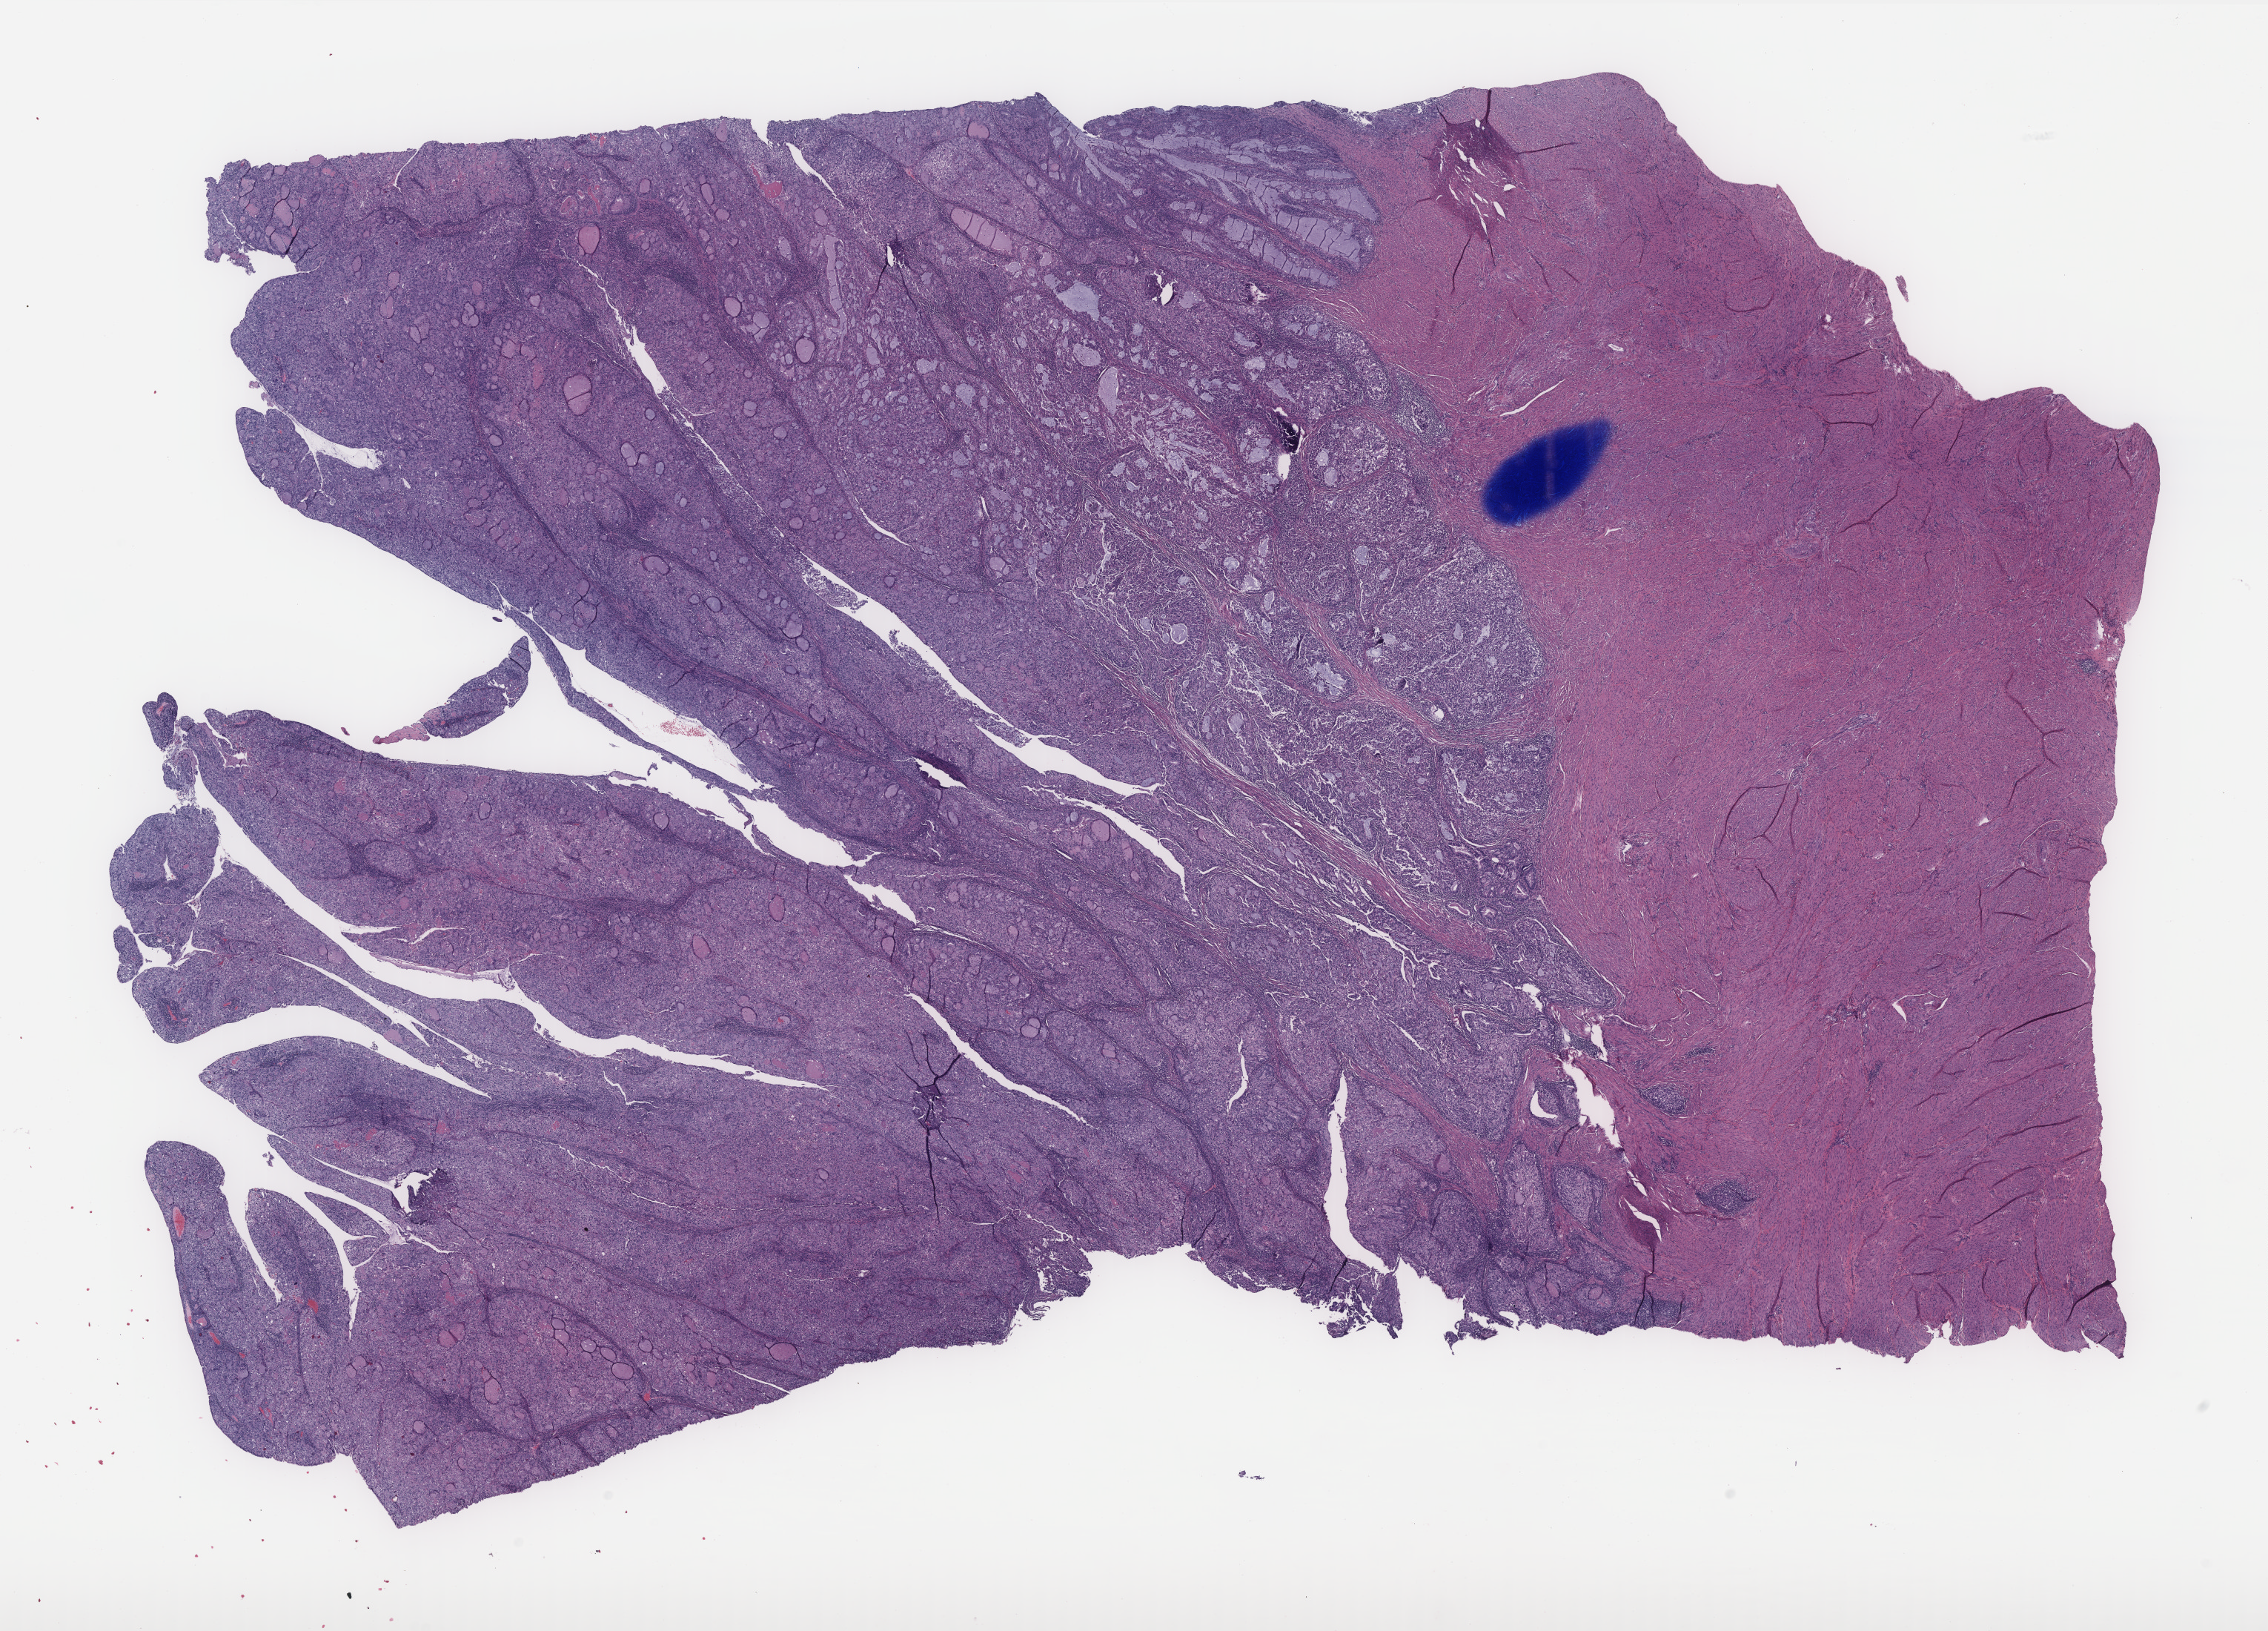
Whole-slide histology image, Hematoxylin and eosin (H&E) stained — a low-resolution overview of the entire scanned area, about 24.5 x 17.6 mm (slide scanned at 40x); formalin-fixed paraffin-embedded (FFPE) diagnostic section; uterus, primary tumour sample. Female, age 50 years at initial diagnosis. Histologic grade: G3 (poorly differentiated).
FIGO stage: IA. Pathologic diagnosis: Endometrioid adenocarcinoma, NOS (endometrium).